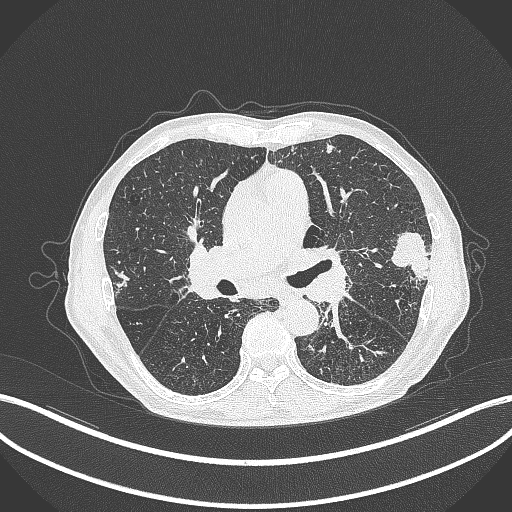
Chest CT, one axial slice; position 232 of 463 along the scan axis; lung window (W 1500 / L -600 HU); 512 × 512 image matrix, field of view 400 × 400 mm. Male patient, age 74 years. Case-level facts recorded for this patient, not image findings: clinical TNM (as recorded): T2a N1 M0.
Annotated regions visible in this slice (rectangle marked by the reading radiologist):
- lung tumour (recorded histology: adenocarcinoma): bounding box [x1, y1, x2, y2] px = [385, 228, 434, 288]